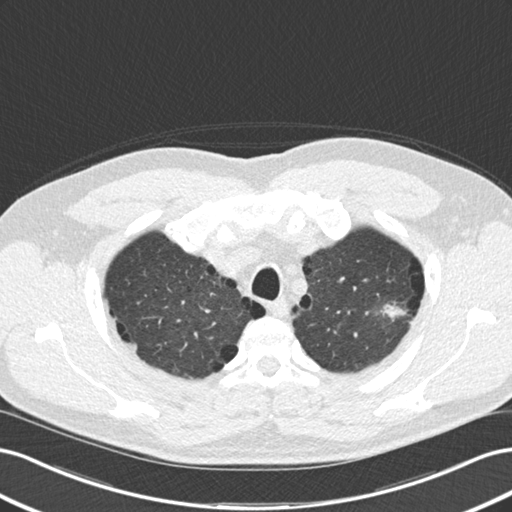
Low-dose screening chest CT, one axial slice. Position 140 of 177 along the scan axis. 120 kVp. Lung window (W 1500 / L -600 HU). 512 × 512 image matrix.
Outlined on this slice (expert manual segmentation):
- lesion 1 (tumor, upper lobe of left lung): bounding box (x1, y1, x2, y2) in pixels: (381, 304, 407, 320)